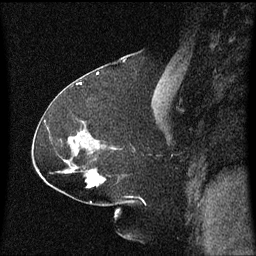
Breast MRI (dynamic contrast-enhanced), one sagittal slice. Slice 31 of 60 in the series (ordered by position). Dynamic contrast-enhanced series, image 2 of 3 at this slice position (ordered by acquisition). 1.5 T. TE 4.2 ms, TR 8 ms. 2.2 mm slice thickness. 256 × 256 image matrix, field of view 200 × 200 mm. Patient: female, 59 years.
Annotated regions visible in this slice (semi-automatically segmented with operator editing):
- analysis volume of interest (the breast-tissue region the enhancement analysis was run in; not a lesion): bounding box (x1, y1, x2, y2) in pixels: (82, 160, 107, 189)
- tumour enhancement mask (voxels above the 70 % enhancement threshold inside the analysis volume of interest): (93, 182, 96, 185)